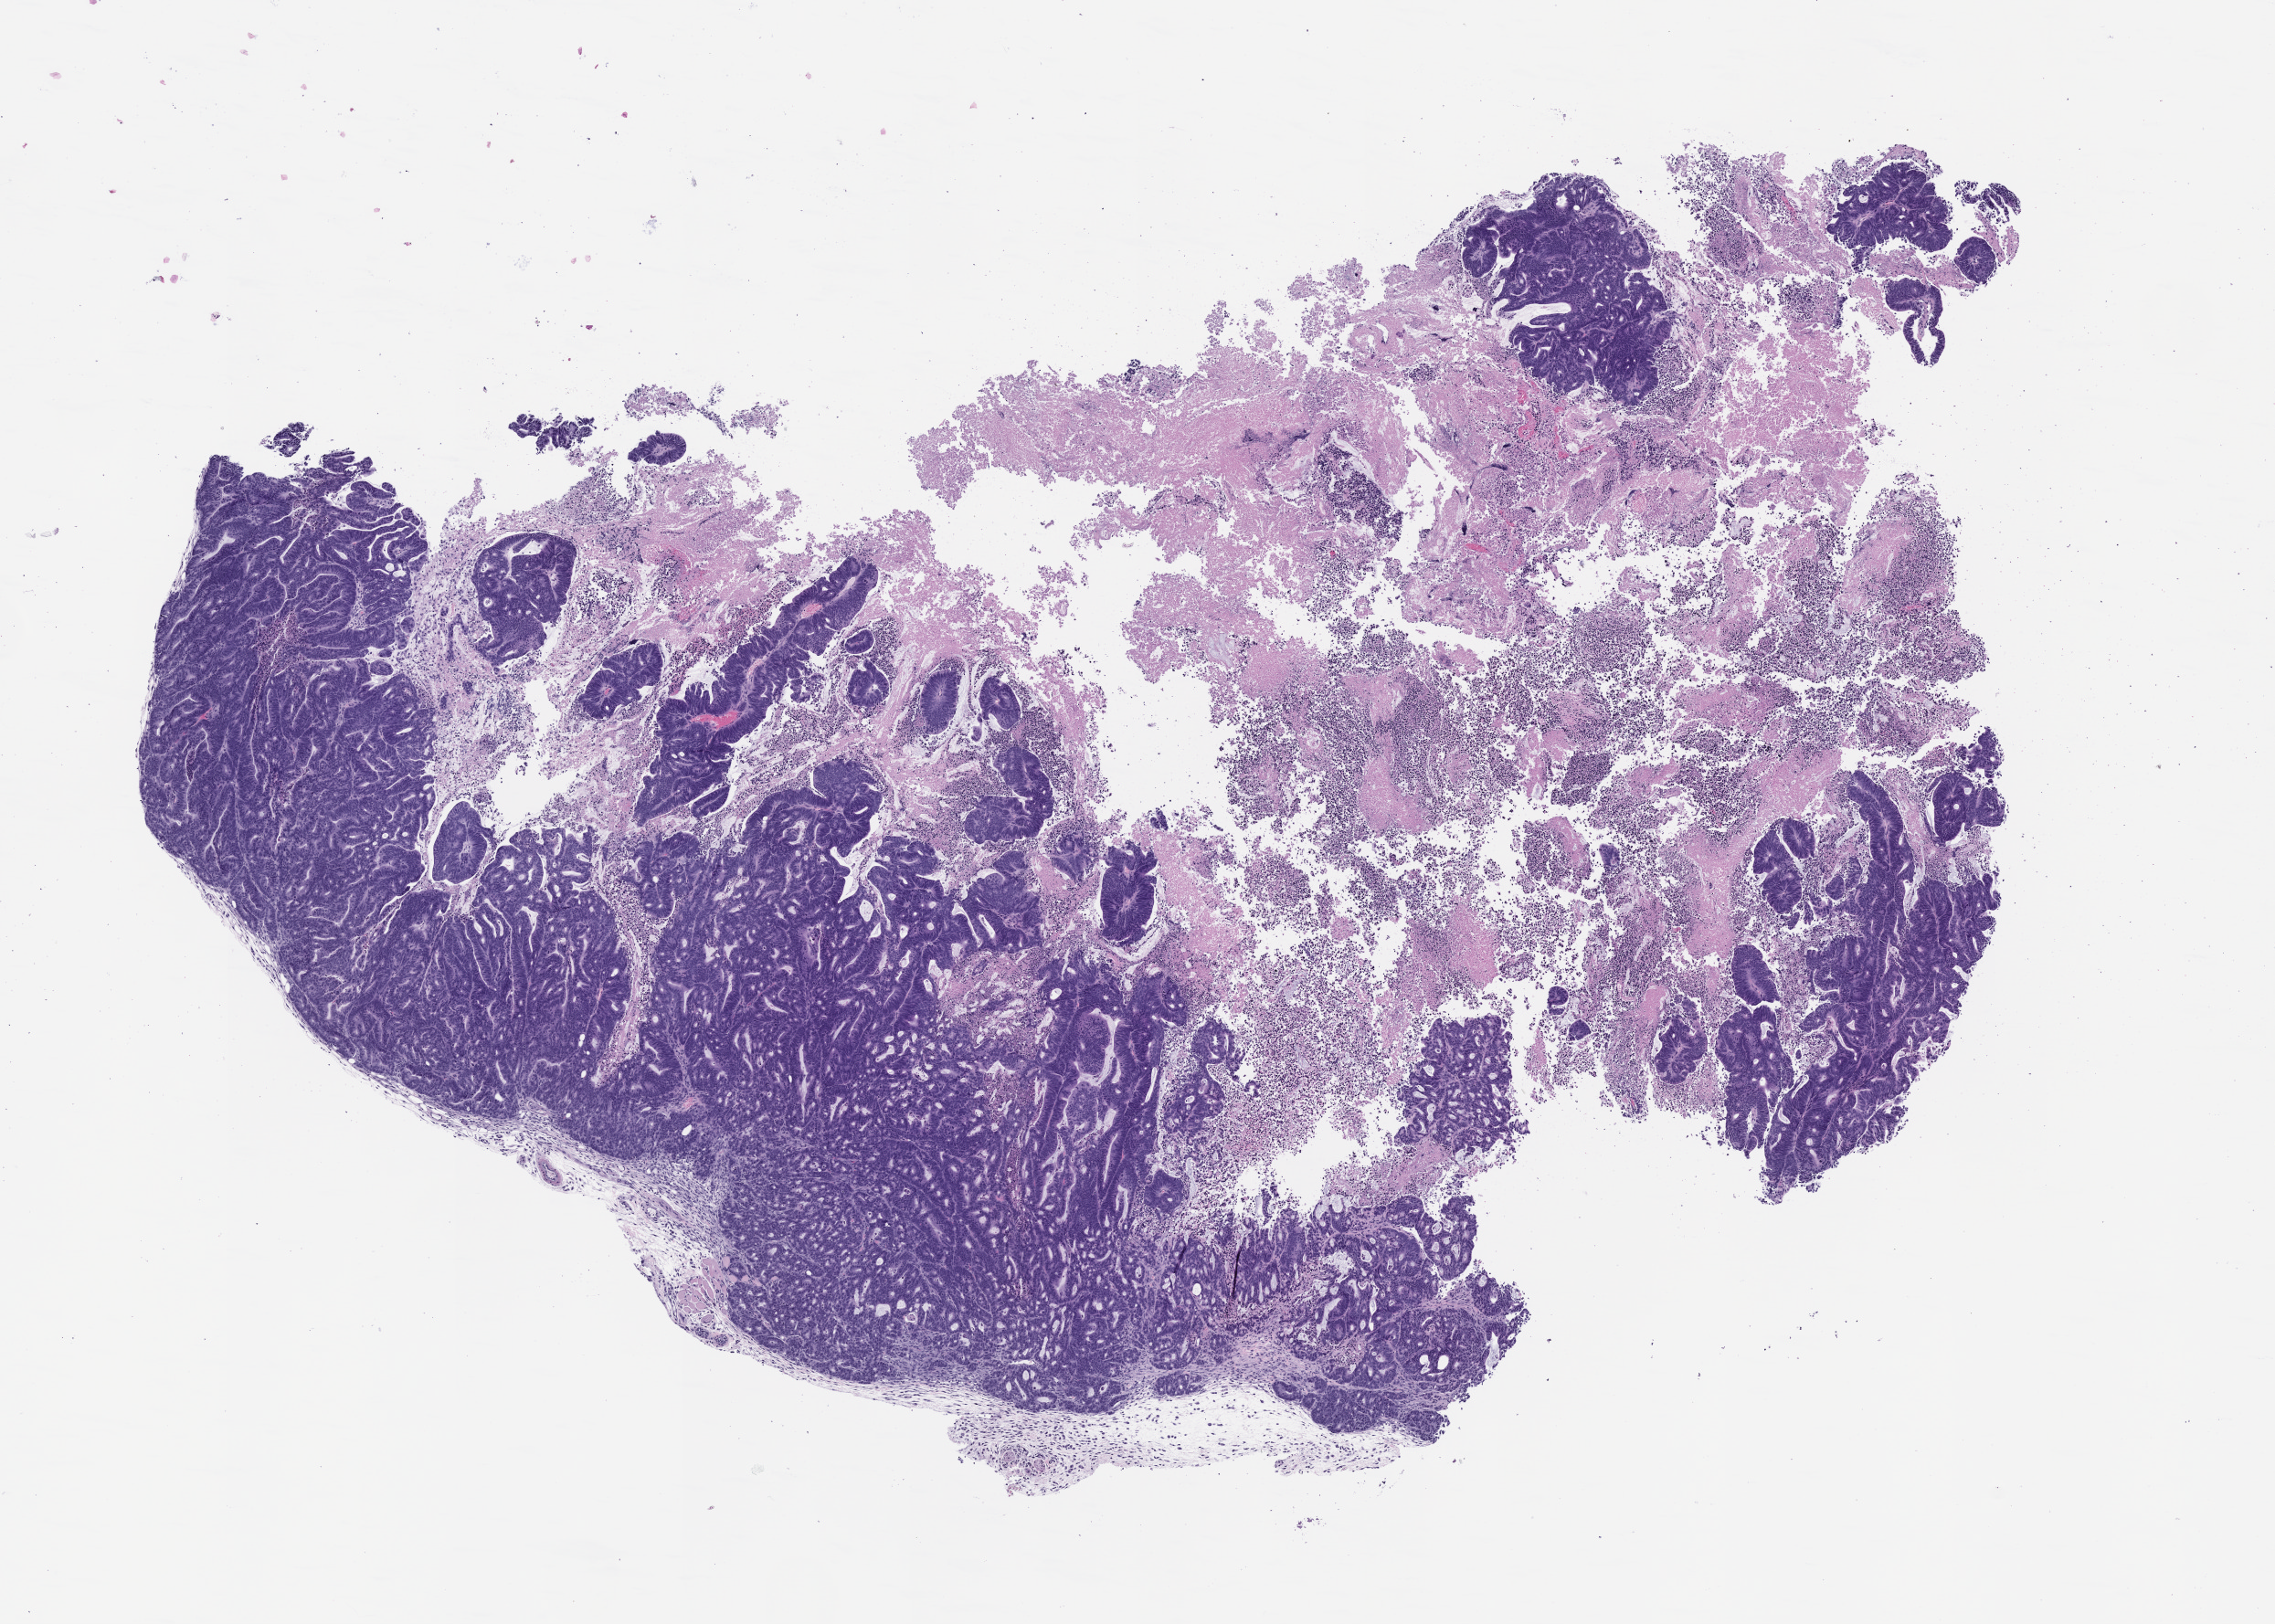
Whole-slide image, H&E: patient-derived xenograft (human tumor grown in a mouse), passage 2, a low-resolution overview of the entire scanned area, about 10.0 x 7.2 mm, FFPE section, tumor site category: colon.
Originating patient diagnosis: Colon Adenocarcinoma.